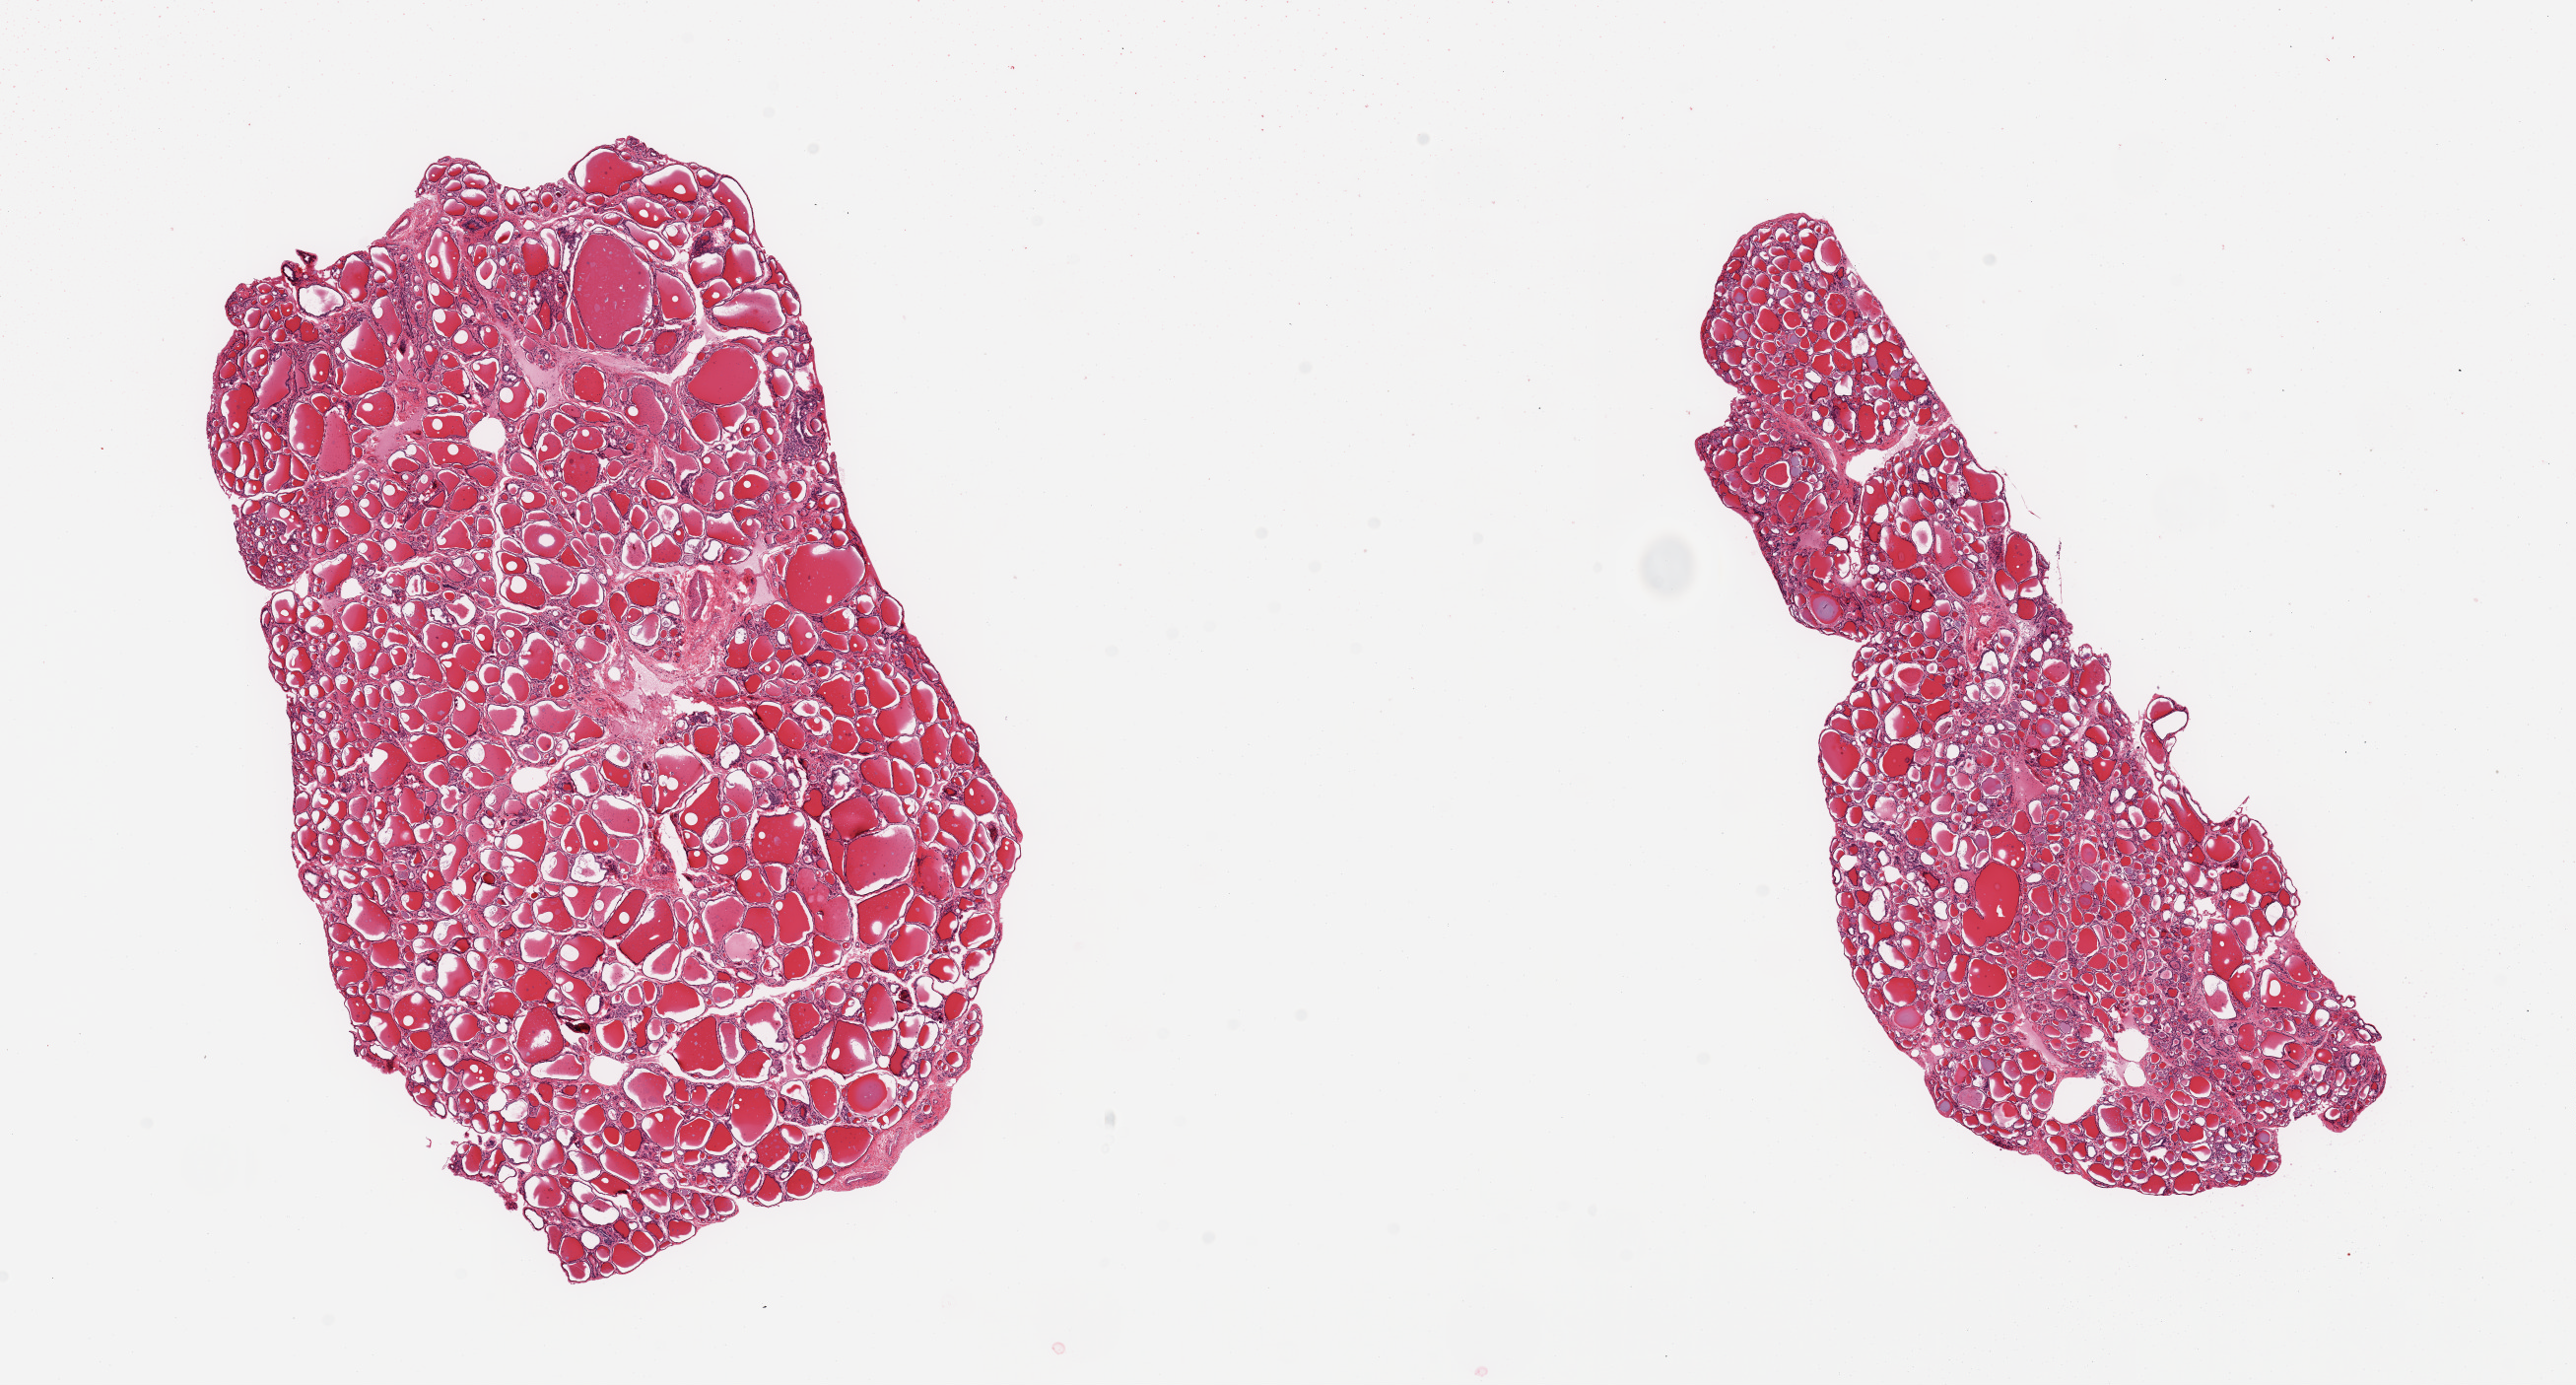
Whole-slide image, haematoxylin and eosin stain — low-resolution overview of the scanned area, about 20.7 x 11.1 mm. PAXgene-fixed paraffin-embedded (PFPE) section. Sampled site (target tissue): thyroid. Tissue donor sample.
Review note (as recorded): 2 pieces, no abnormalities.